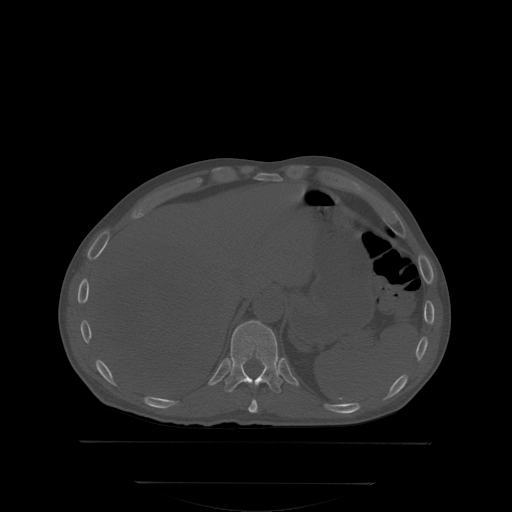
CT including the spine, one axial slice. Slice 183 of 350 in the series (ordered by position). Bone window (W 1800 / L 400 HU). 512 × 512 image matrix, field of view 500 × 500 mm. Male patient, age 58 years. From the clinical record (not read from this slice): primary cancer: prostate.
Structures marked on this image (semi-automatically segmented with operator editing):
- T10 vertebra: bounding box <248,398,258,412> (left, top, right, bottom; pixels)
- T11 vertebra: <224,320,282,393>